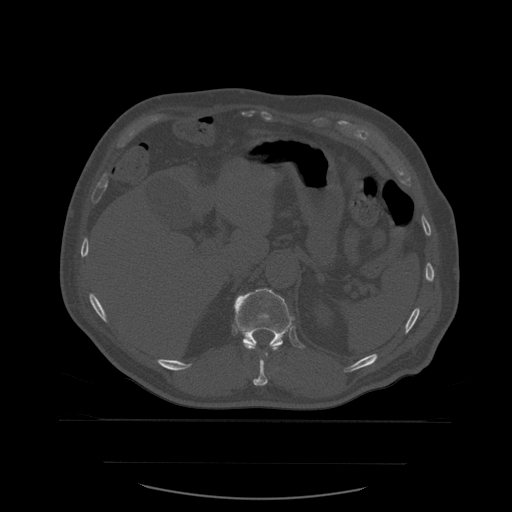
CT including the spine, one axial slice. Slice 282 of 590 in the series (ordered by position). Bone window (W 1800 / L 400 HU). 1.25 mm slice thickness. 512 × 512 image matrix, field of view 479 × 479 mm. Patient age 71 years. From the clinical record (not read from this slice): primary cancer: lung; vertebrae with lytic lesions (as recorded): T1, T2, L5, S1.
Outlined on this slice (semi-automatic segmentation, software-assisted and operator-edited):
- T11 vertebra: bounding box <244,344,281,386> (left, top, right, bottom; pixels)
- T12 vertebra: <234,289,295,349>